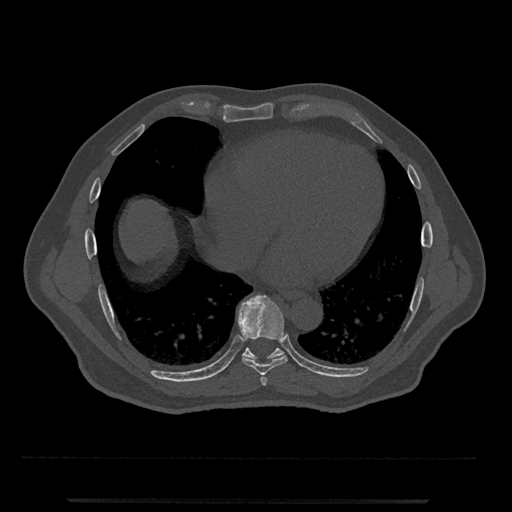
CT including the spine, one axial slice. Slice 609 of 797 in the series (ordered by position). 120 kVp. Bone window (W 1800 / L 400 HU). 512 × 512 image matrix, field of view 419 × 419 mm. Male patient, age 63 years. Case-level facts recorded for this patient, not image findings: primary cancer: prostate.
Annotated regions visible in this slice (semi-automatically segmented with operator editing):
- T7 vertebra: bounding box (x1, y1, x2, y2) in pixels: (260, 375, 267, 386)
- T8 vertebra: (238, 295, 288, 375)
- T9 vertebra: (242, 338, 284, 361)